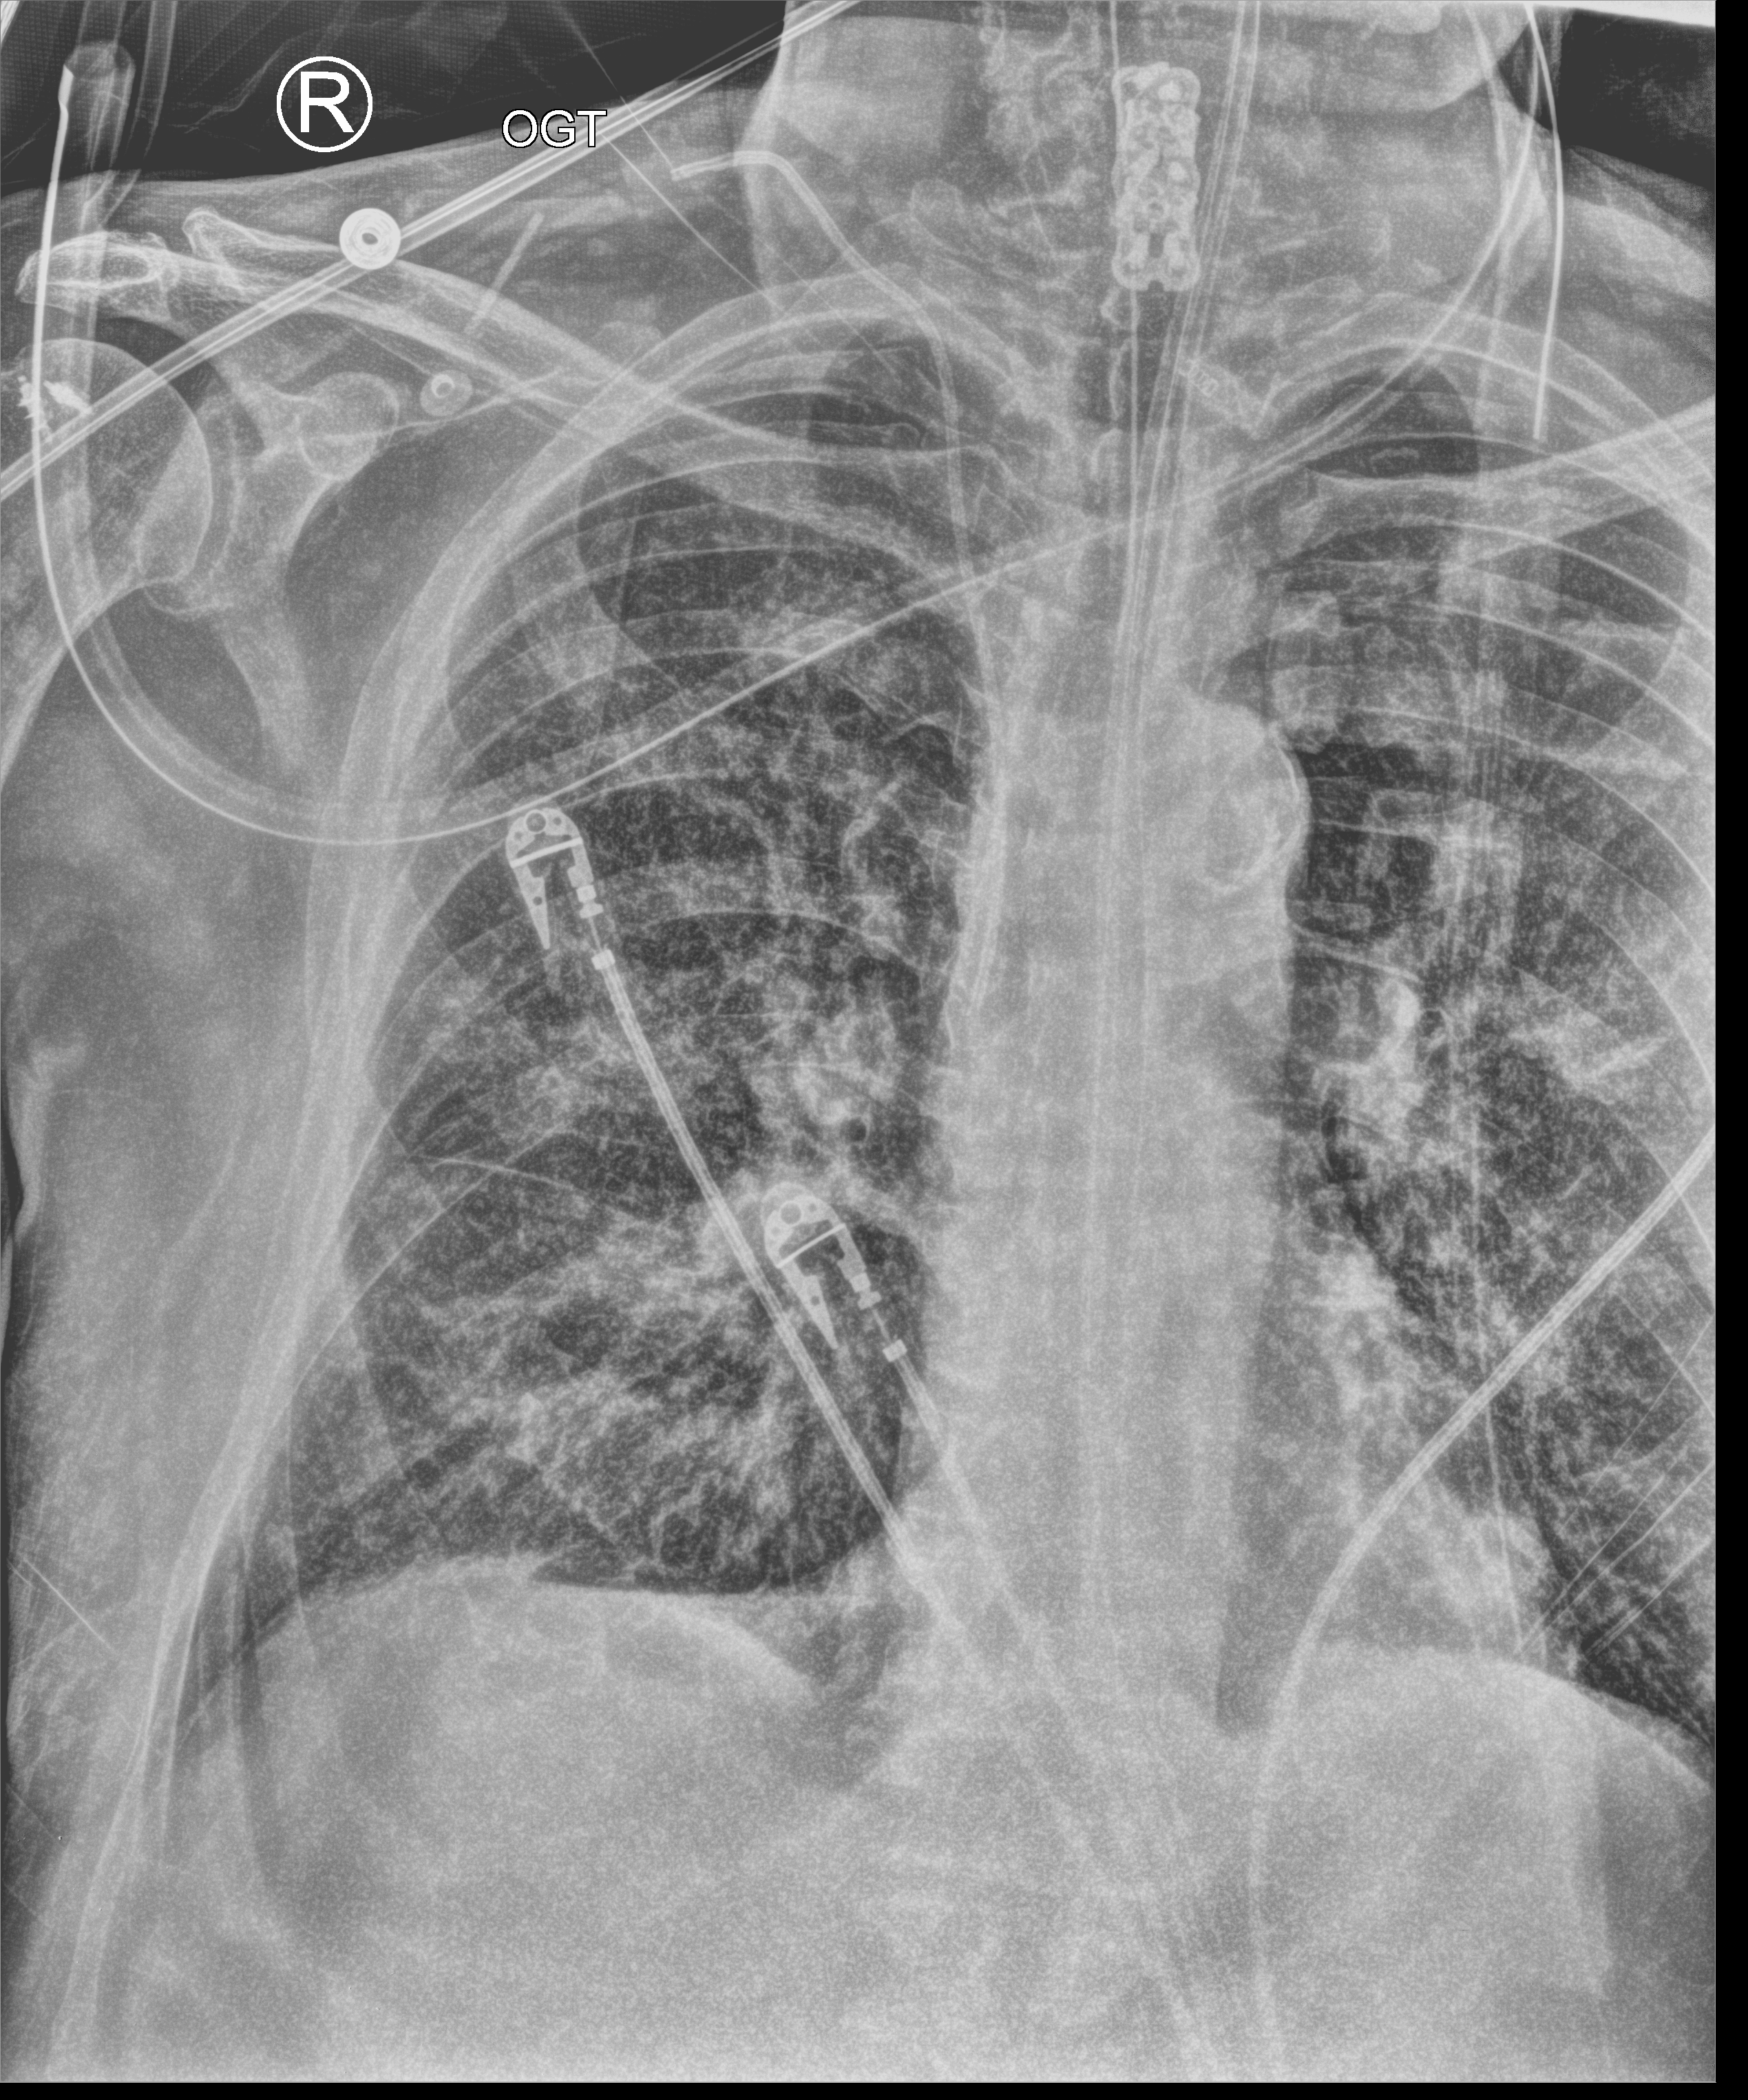
Chest X-ray (portable), anteroposterior (AP) projection. Patient hospitalised with COVID-19; male, aged 75–90 years.
From the hospital-stay record, not from the radiograph (when in the stay this image was taken is not recorded):
- mechanically ventilated during this hospital stay: yes
- length of hospital stay: 26 days
- chronic kidney disease (admission record): no